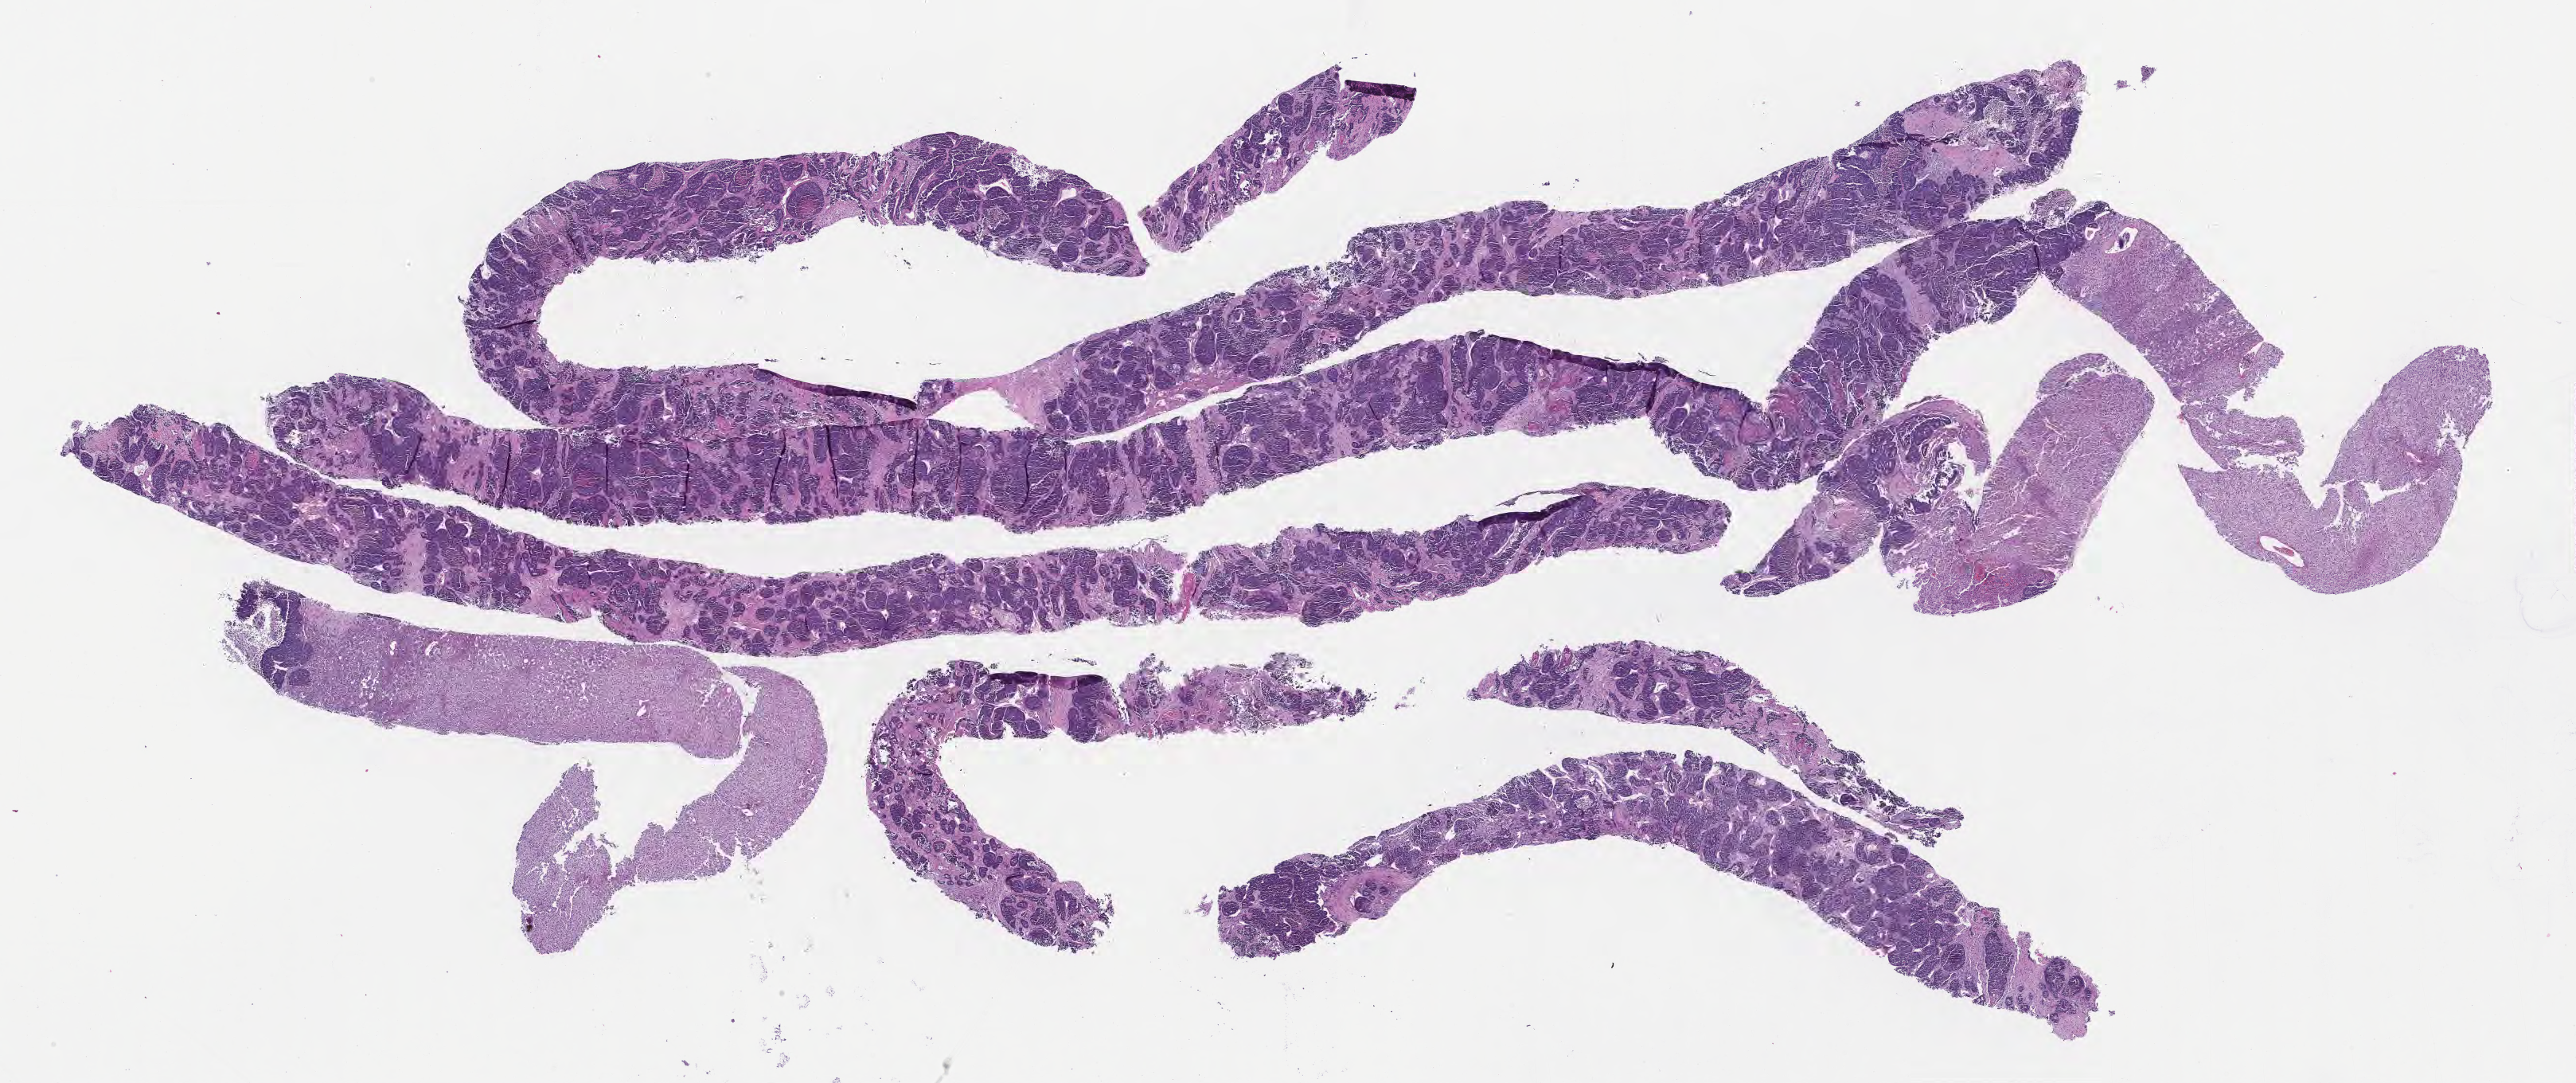
Digitized haematoxylin and eosin-stained section of tumor tissue — whole scanned area (about 26.2 x 11.0 mm) shown as a low-resolution overview. Formalin-fixed, paraffin-embedded (FFPE) tissue. Patient male; age 105 months.
• recorded diagnosis: Carcinoma, metastatic, NOS